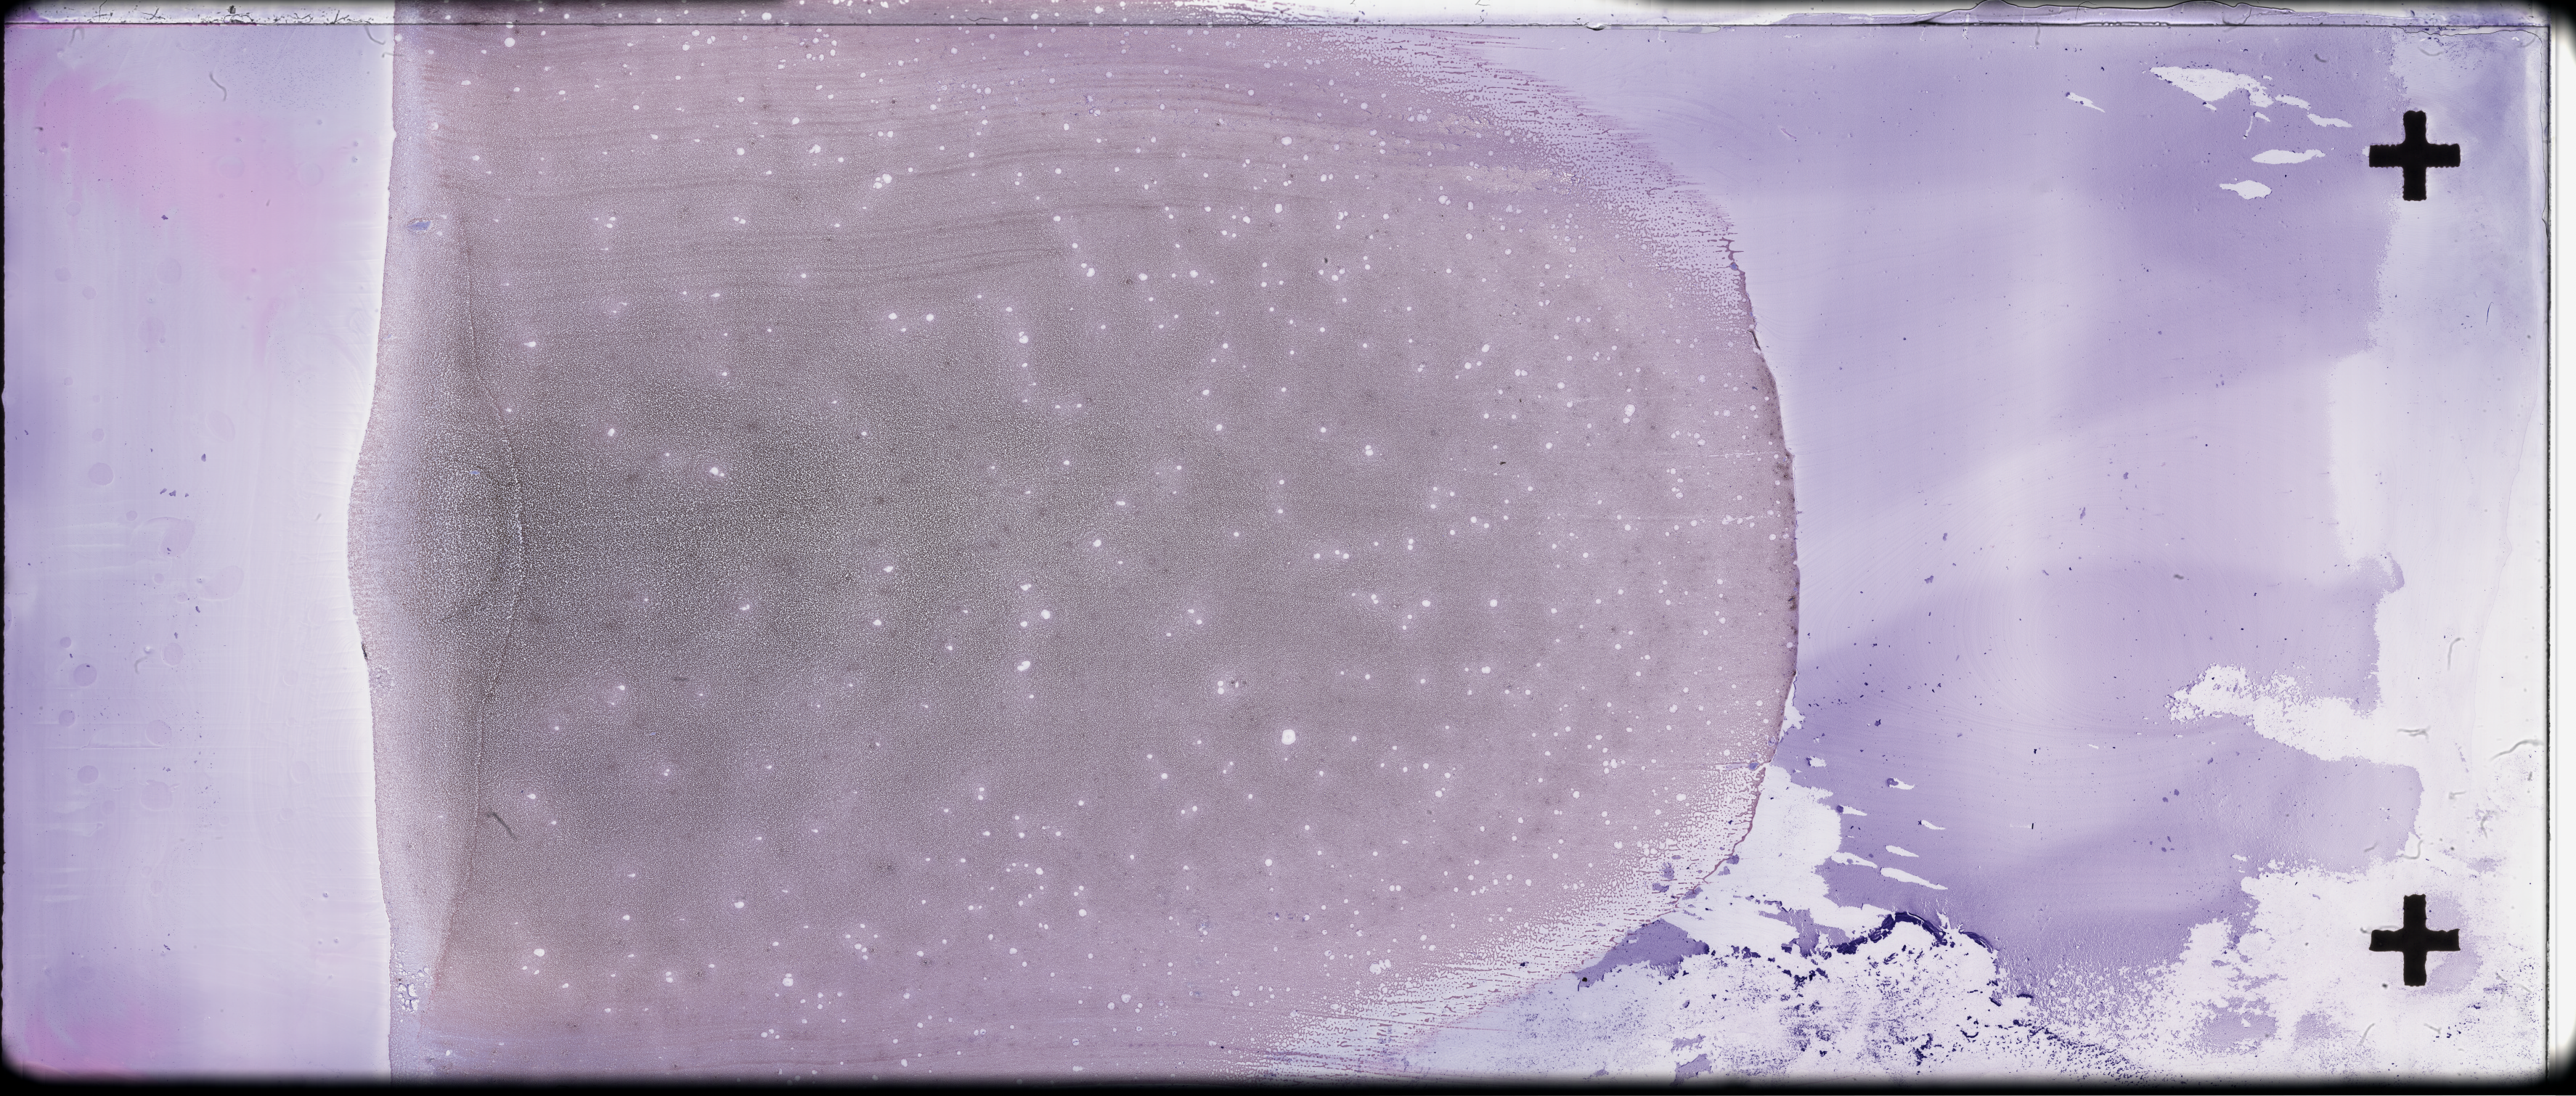
Wright–Giemsa-stained whole blood smear, whole-slide image — a low-resolution overview of the entire scanned area, about 57.3 x 24.4 mm. Patient: female.
* patient diagnosis: Plasma Cell Myeloma